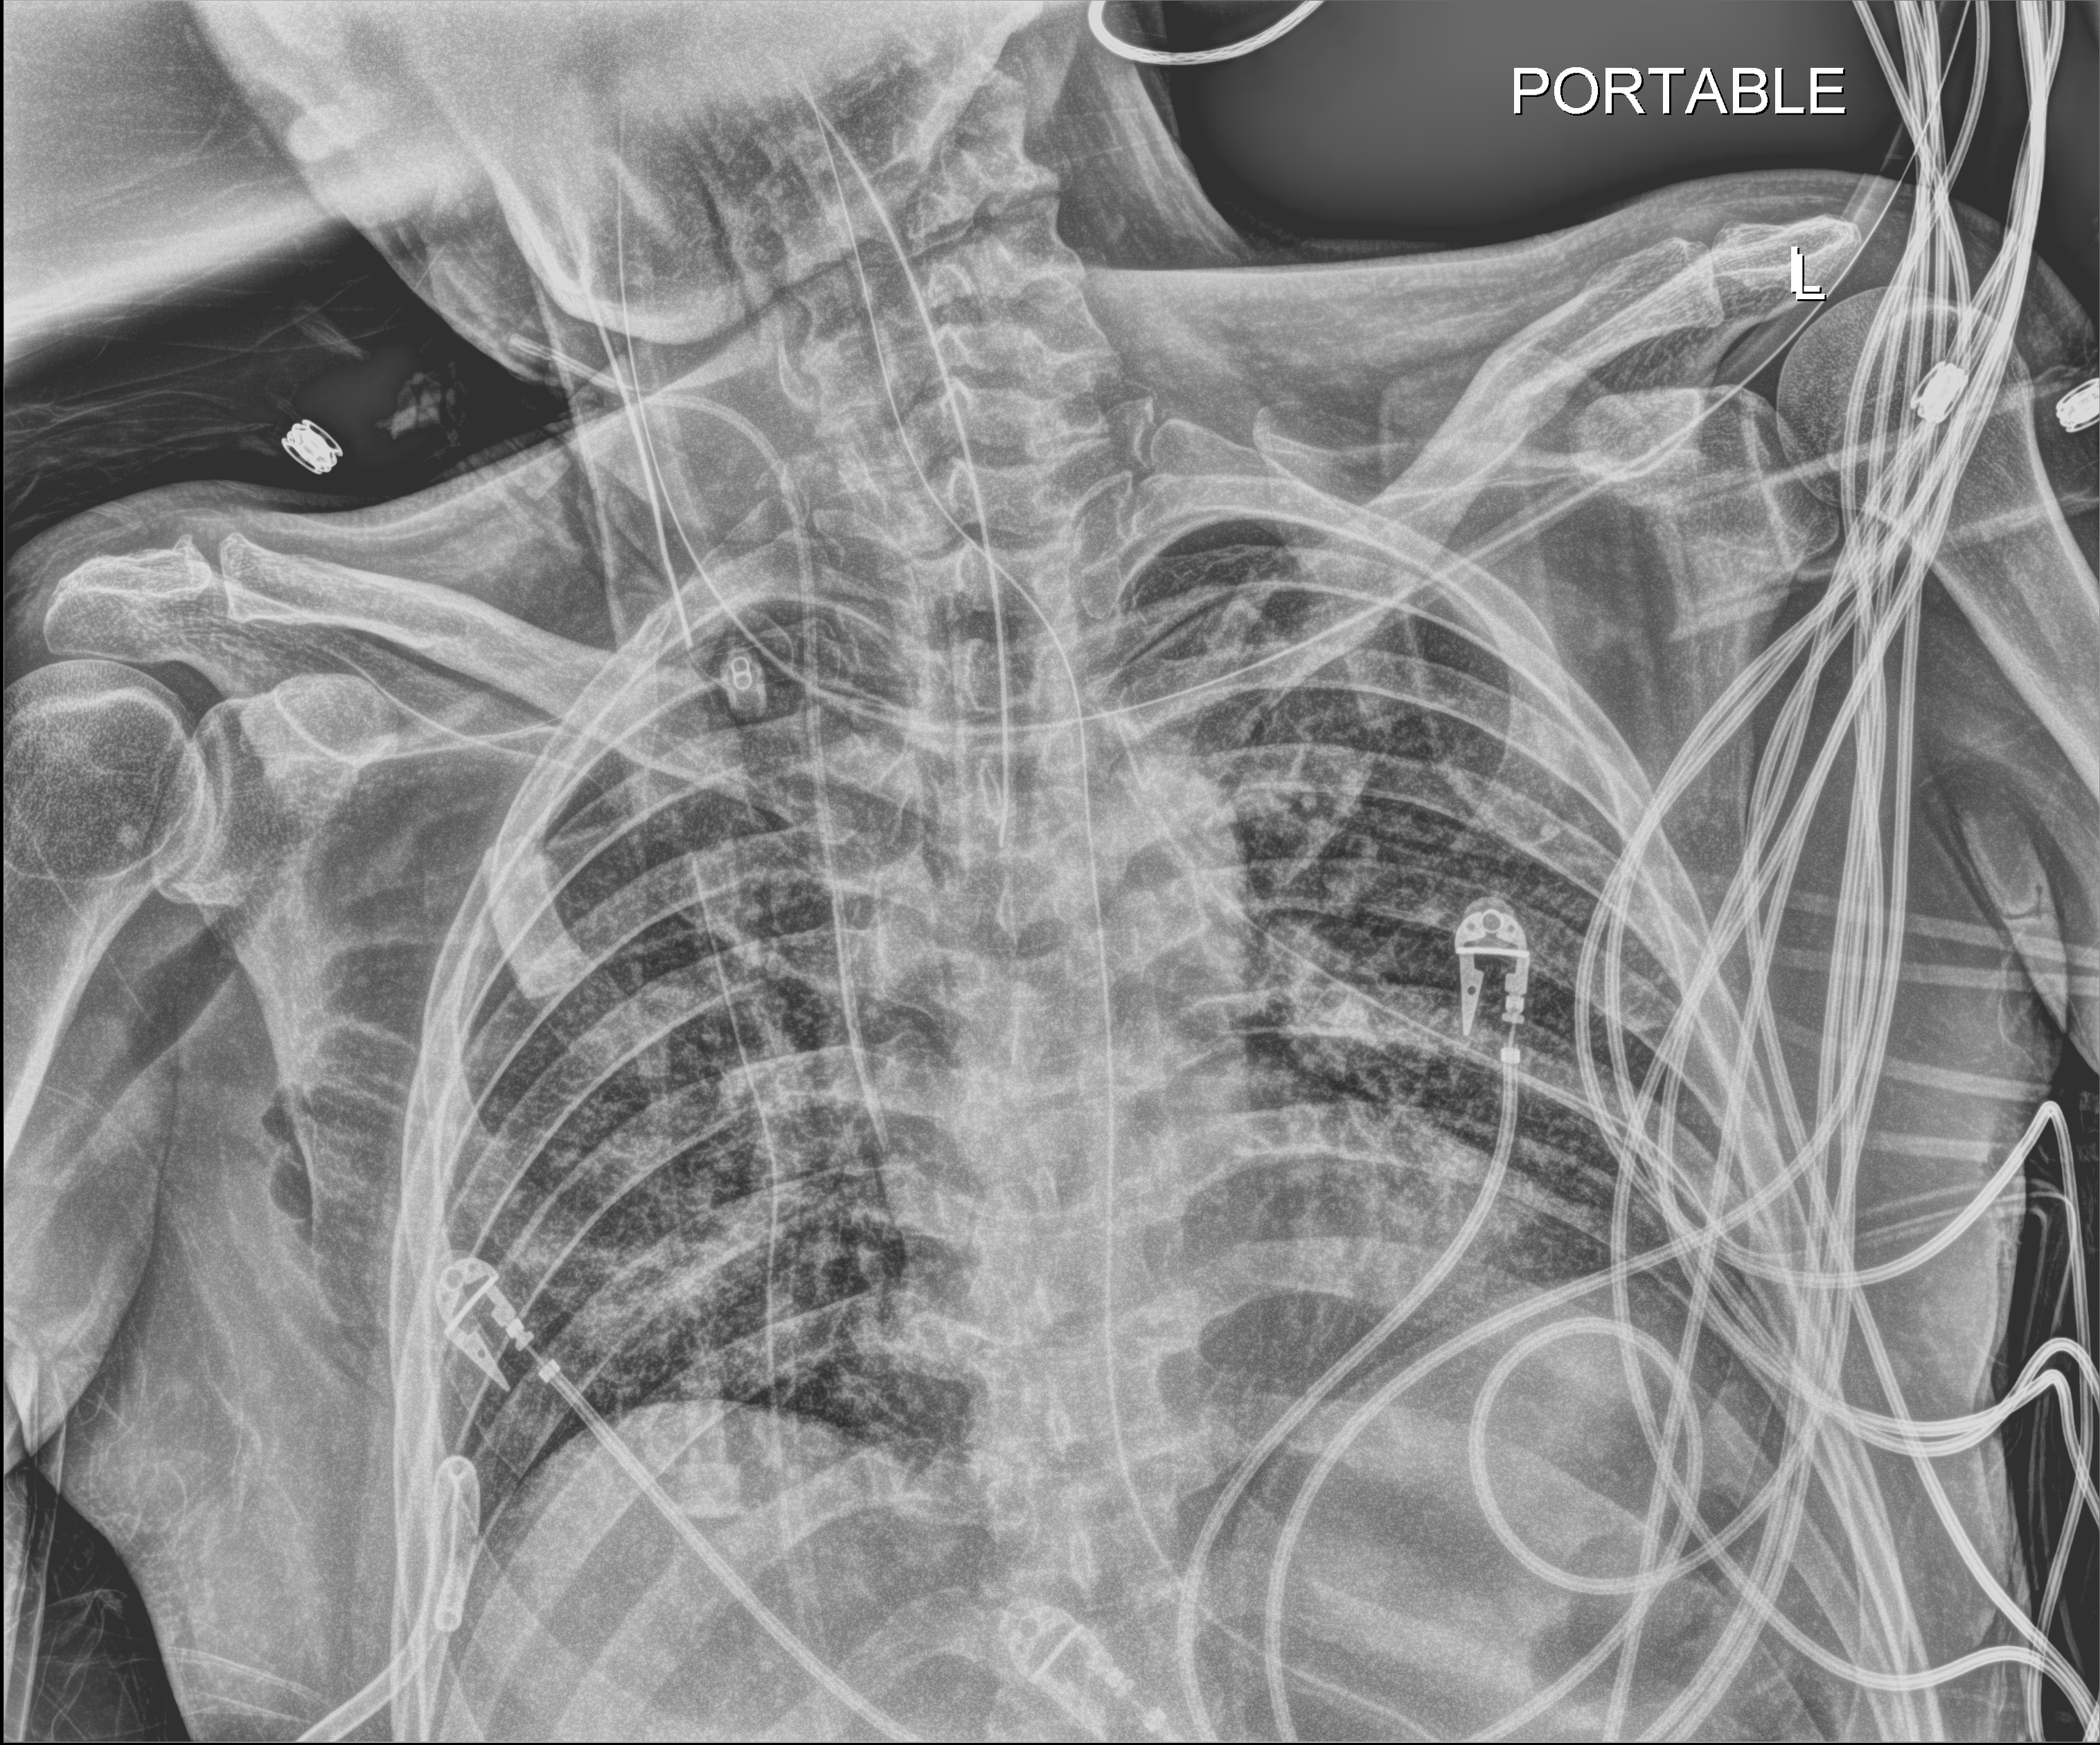
Portable chest radiograph, anteroposterior (AP) projection. Patient hospitalised with COVID-19; male, aged 18–59 years.
Admission-level facts for this patient (not findings on this image; timing relative to this image not recorded): mechanically ventilated during this hospital stay: yes.